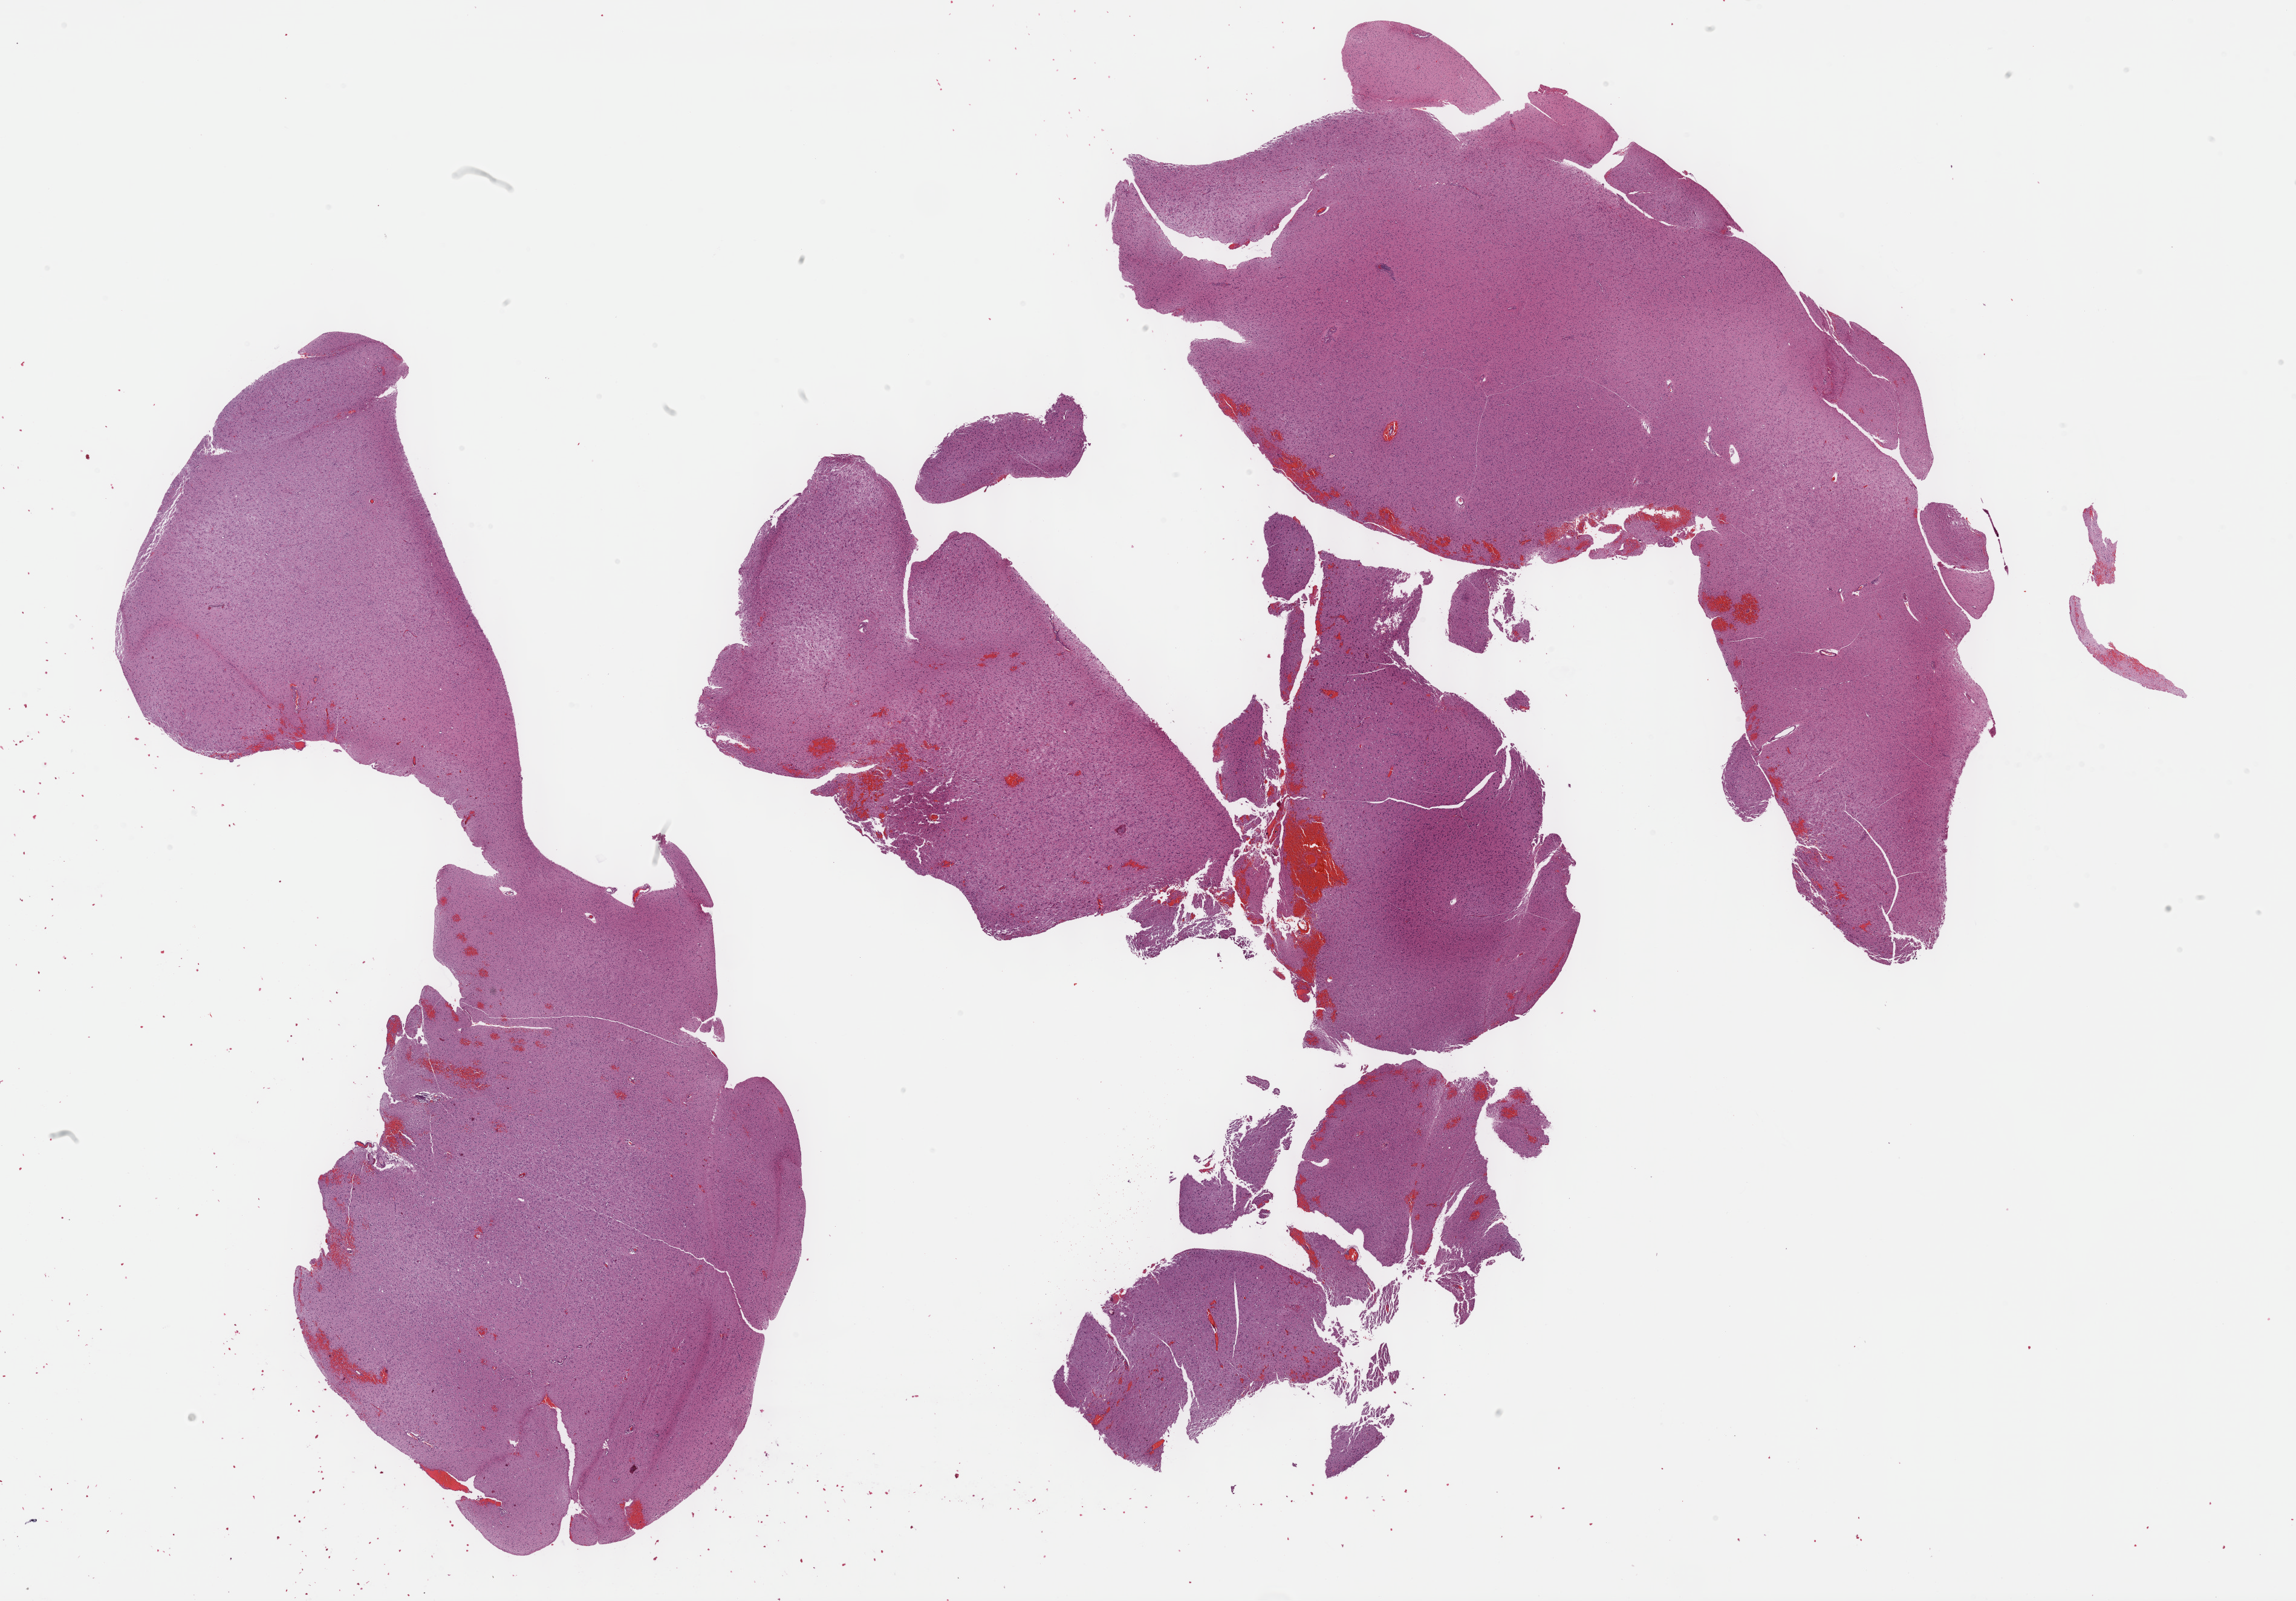
Digitized H&E tissue section (whole slide) — low-resolution overview of the scanned area, about 30.7 x 21.4 mm; formalin-fixed paraffin-embedded (FFPE) diagnostic section; sample: primary tumour, brain. Patient: female, age at initial diagnosis 30 years. Histologic grade: G3 (poorly differentiated).
Pathologic diagnosis: Astrocytoma, anaplastic.